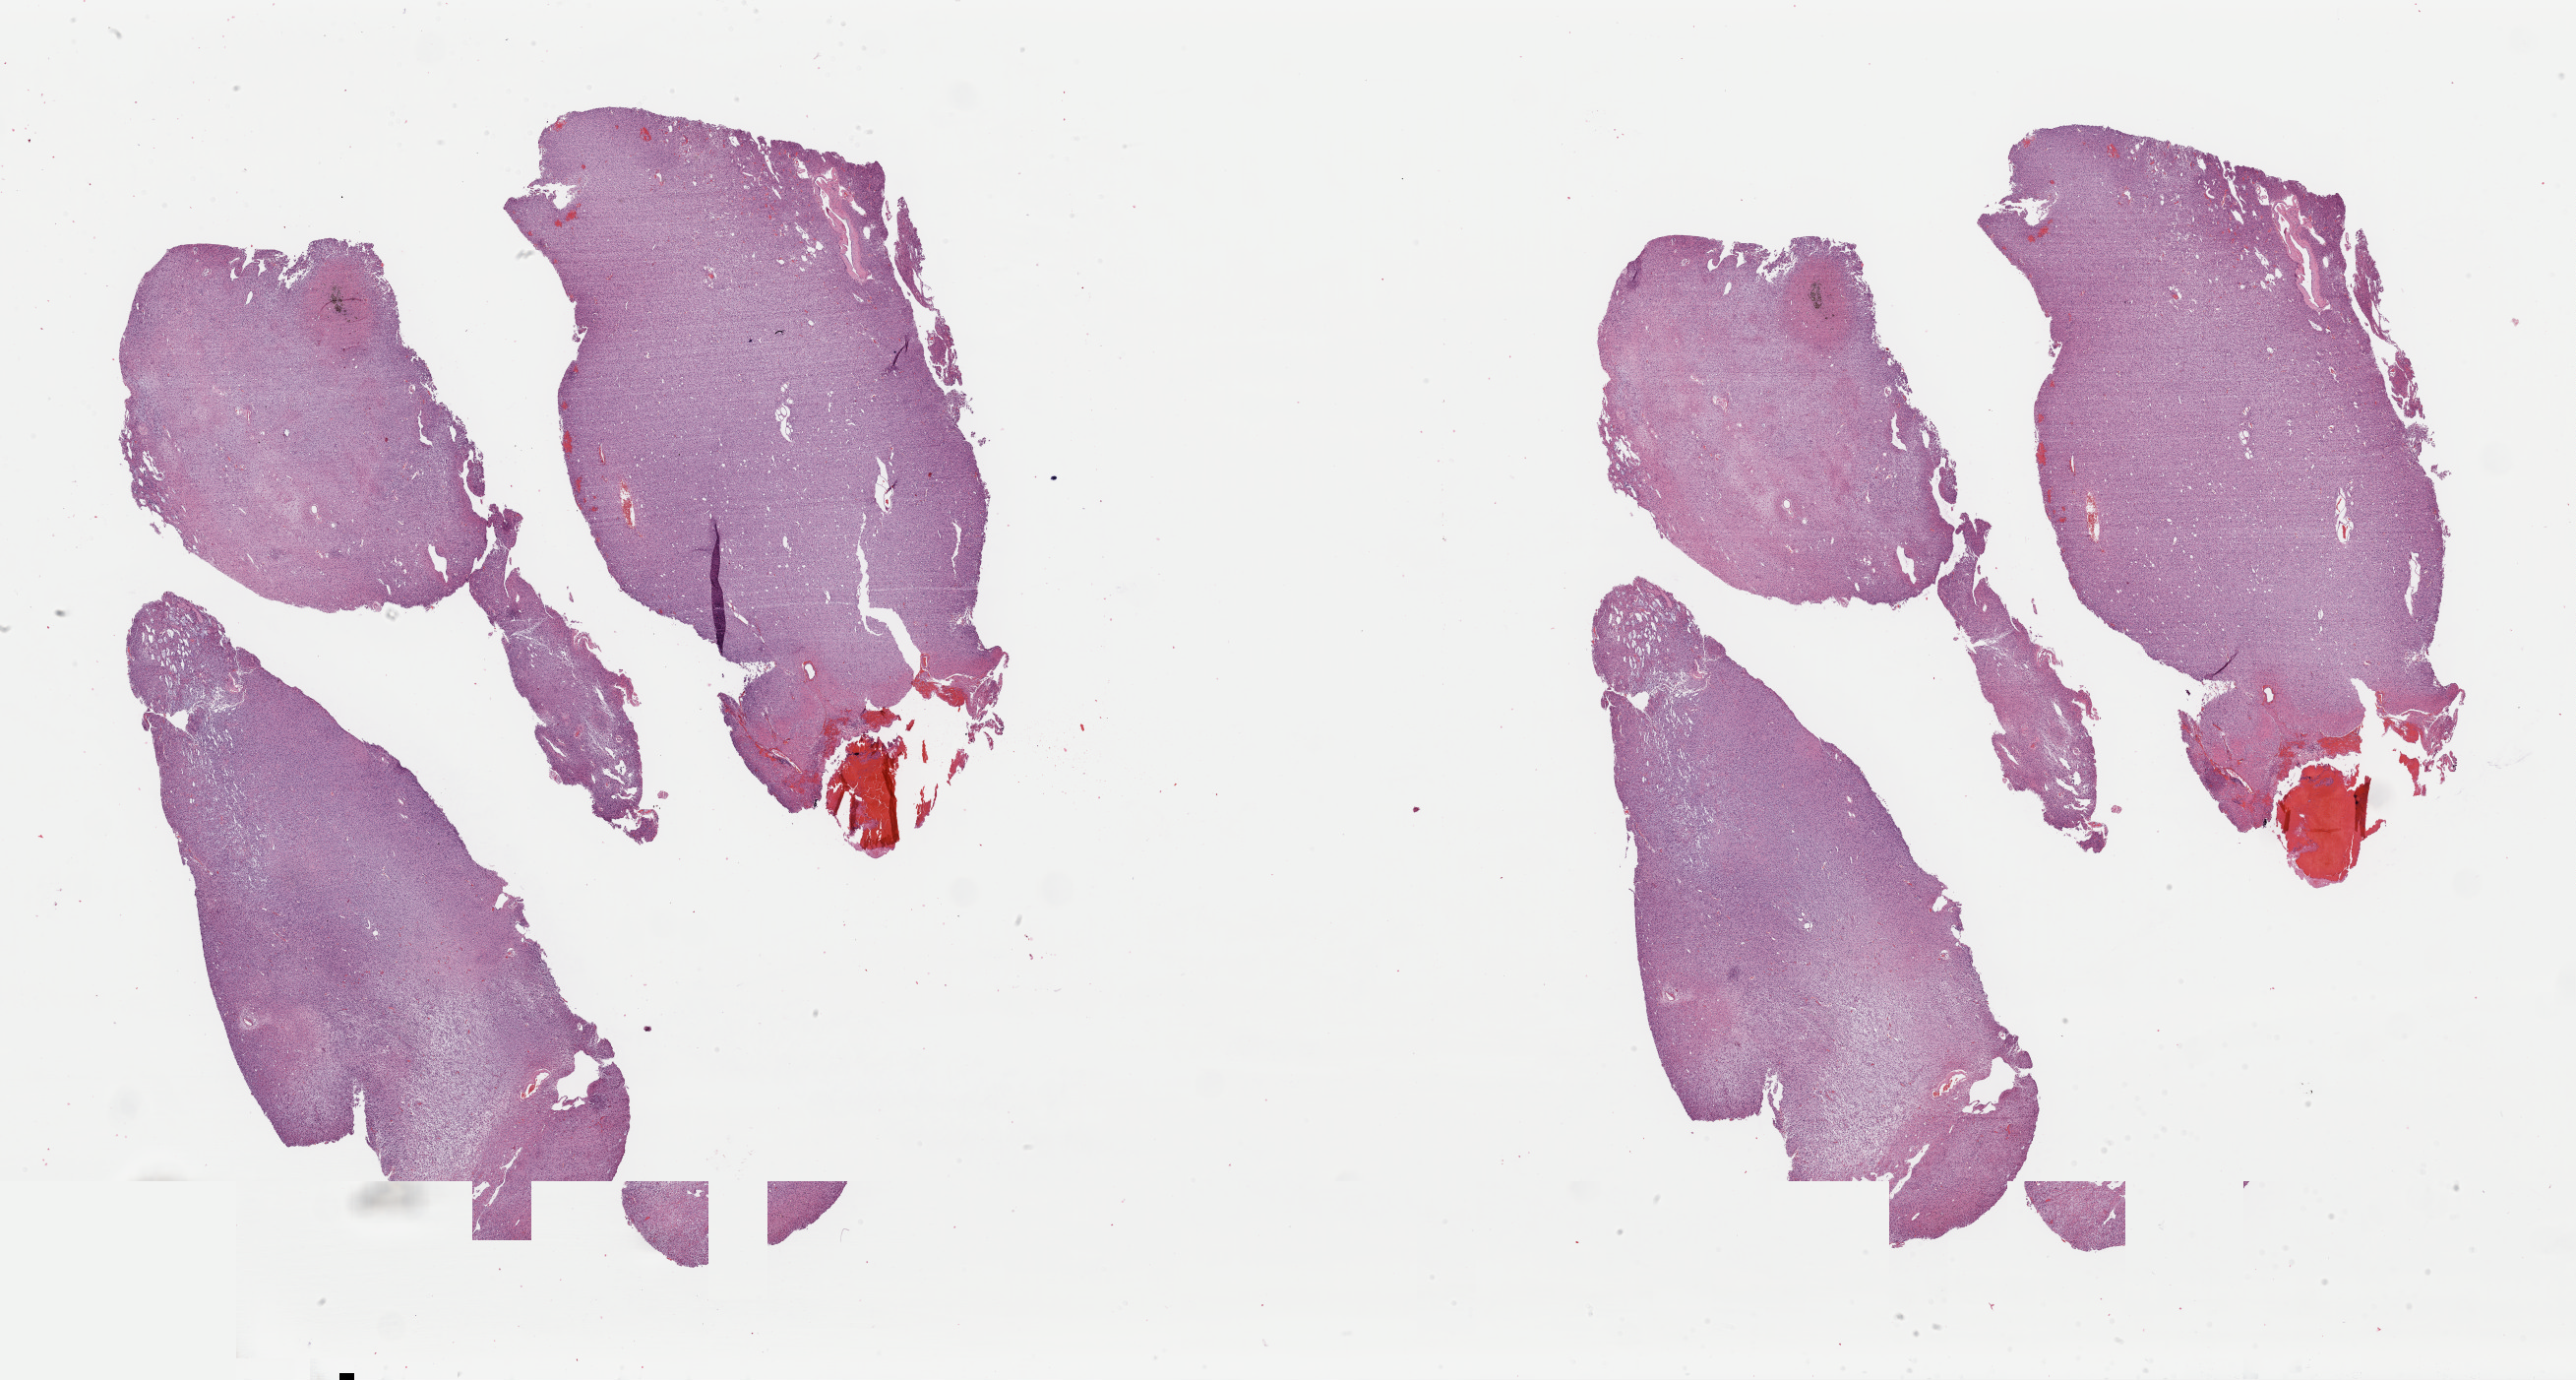
Digitized H&E tissue section (whole slide) — whole scanned area (about 41.4 x 22.1 mm, acquisition: 40x scan) shown as a low-resolution overview. Formalin-fixed paraffin-embedded (FFPE) diagnostic section. Primary tumour sample from the brain. Patient: male, age at initial diagnosis 47 years. Histologic grade: G2 (moderately differentiated).
Histologic diagnosis: Astrocytoma, NOS (frontal lobe).